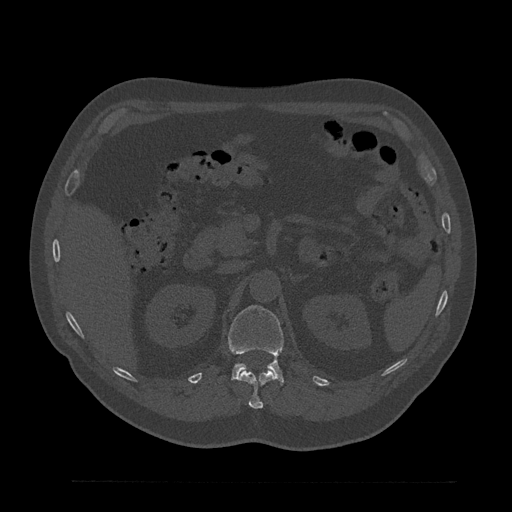
CT including the spine, one axial slice; slice 193 of 797 in the series (ordered by position); reconstruction kernel Br40s/3; 120 kVp; bone window (W 1800 / L 400 HU); 0.5 mm slice thickness; 512 × 512 image matrix, field of view 430 × 430 mm. Patient: male, 61 years. From the clinical record (not read from this slice): primary cancer: prostate.
Annotated regions visible in this slice (semi-automatic segmentation, software-assisted and operator-edited):
- L1 vertebra: bounding box [x1, y1, x2, y2] px = [228, 305, 284, 384]
- T12 vertebra: [237, 369, 276, 409]